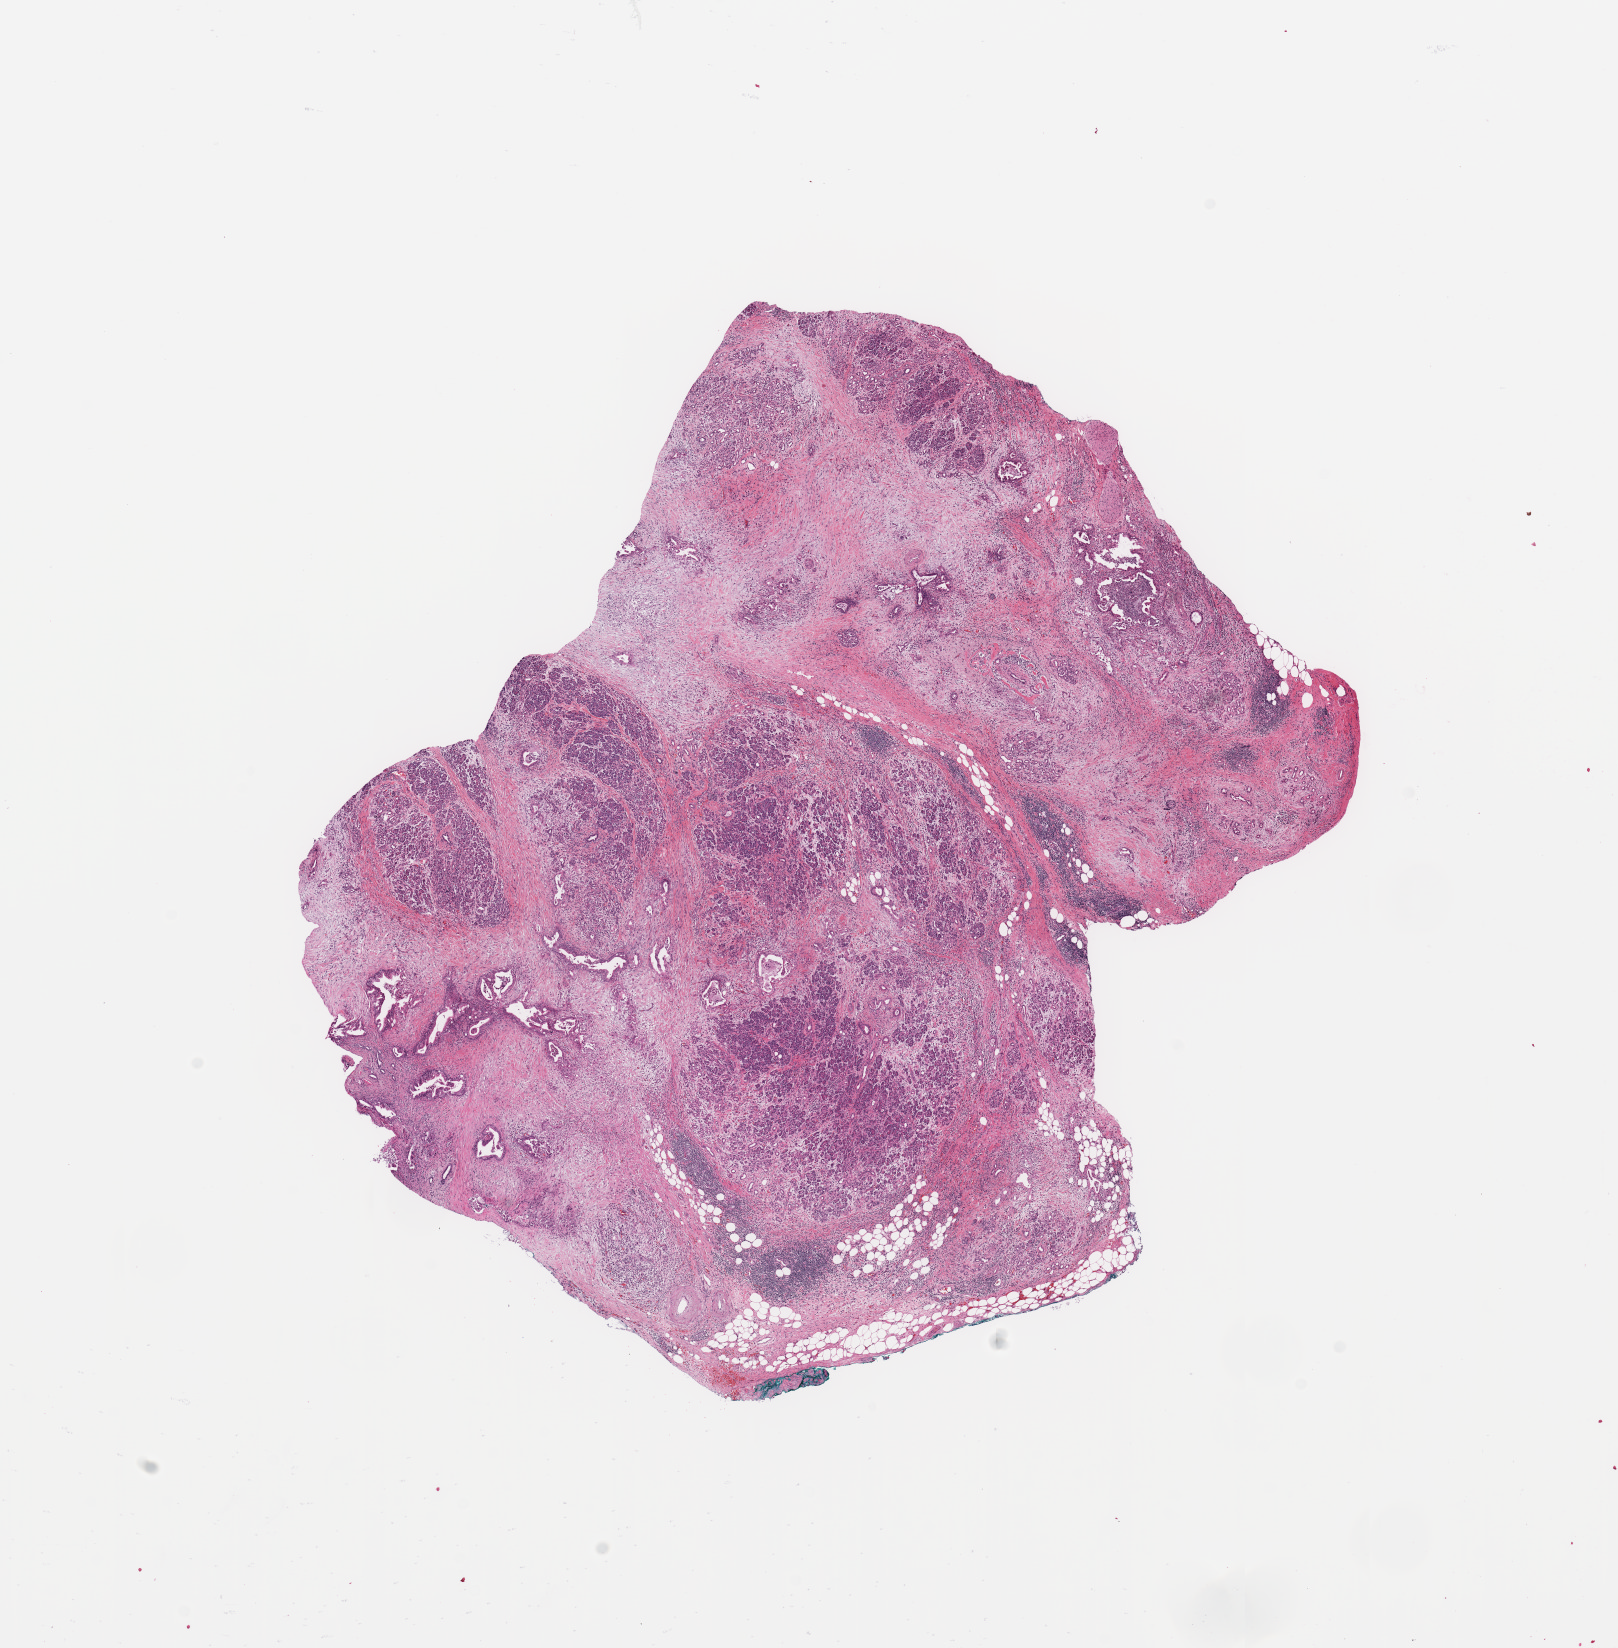
Whole-slide histology image, Hematoxylin and eosin (H&E) stained, shown as a low-resolution overview of the whole scanned area (about 12.8 x 13.0 mm, from a 20x scan); pancreas, tumour tissue. 76-year-old female patient. Histologic grade: G2 (moderately differentiated).
- primary tumour site (as recorded): head
- AJCC pathologic stage: IIB
- diagnosis: Infiltrating duct carcinoma, NOS